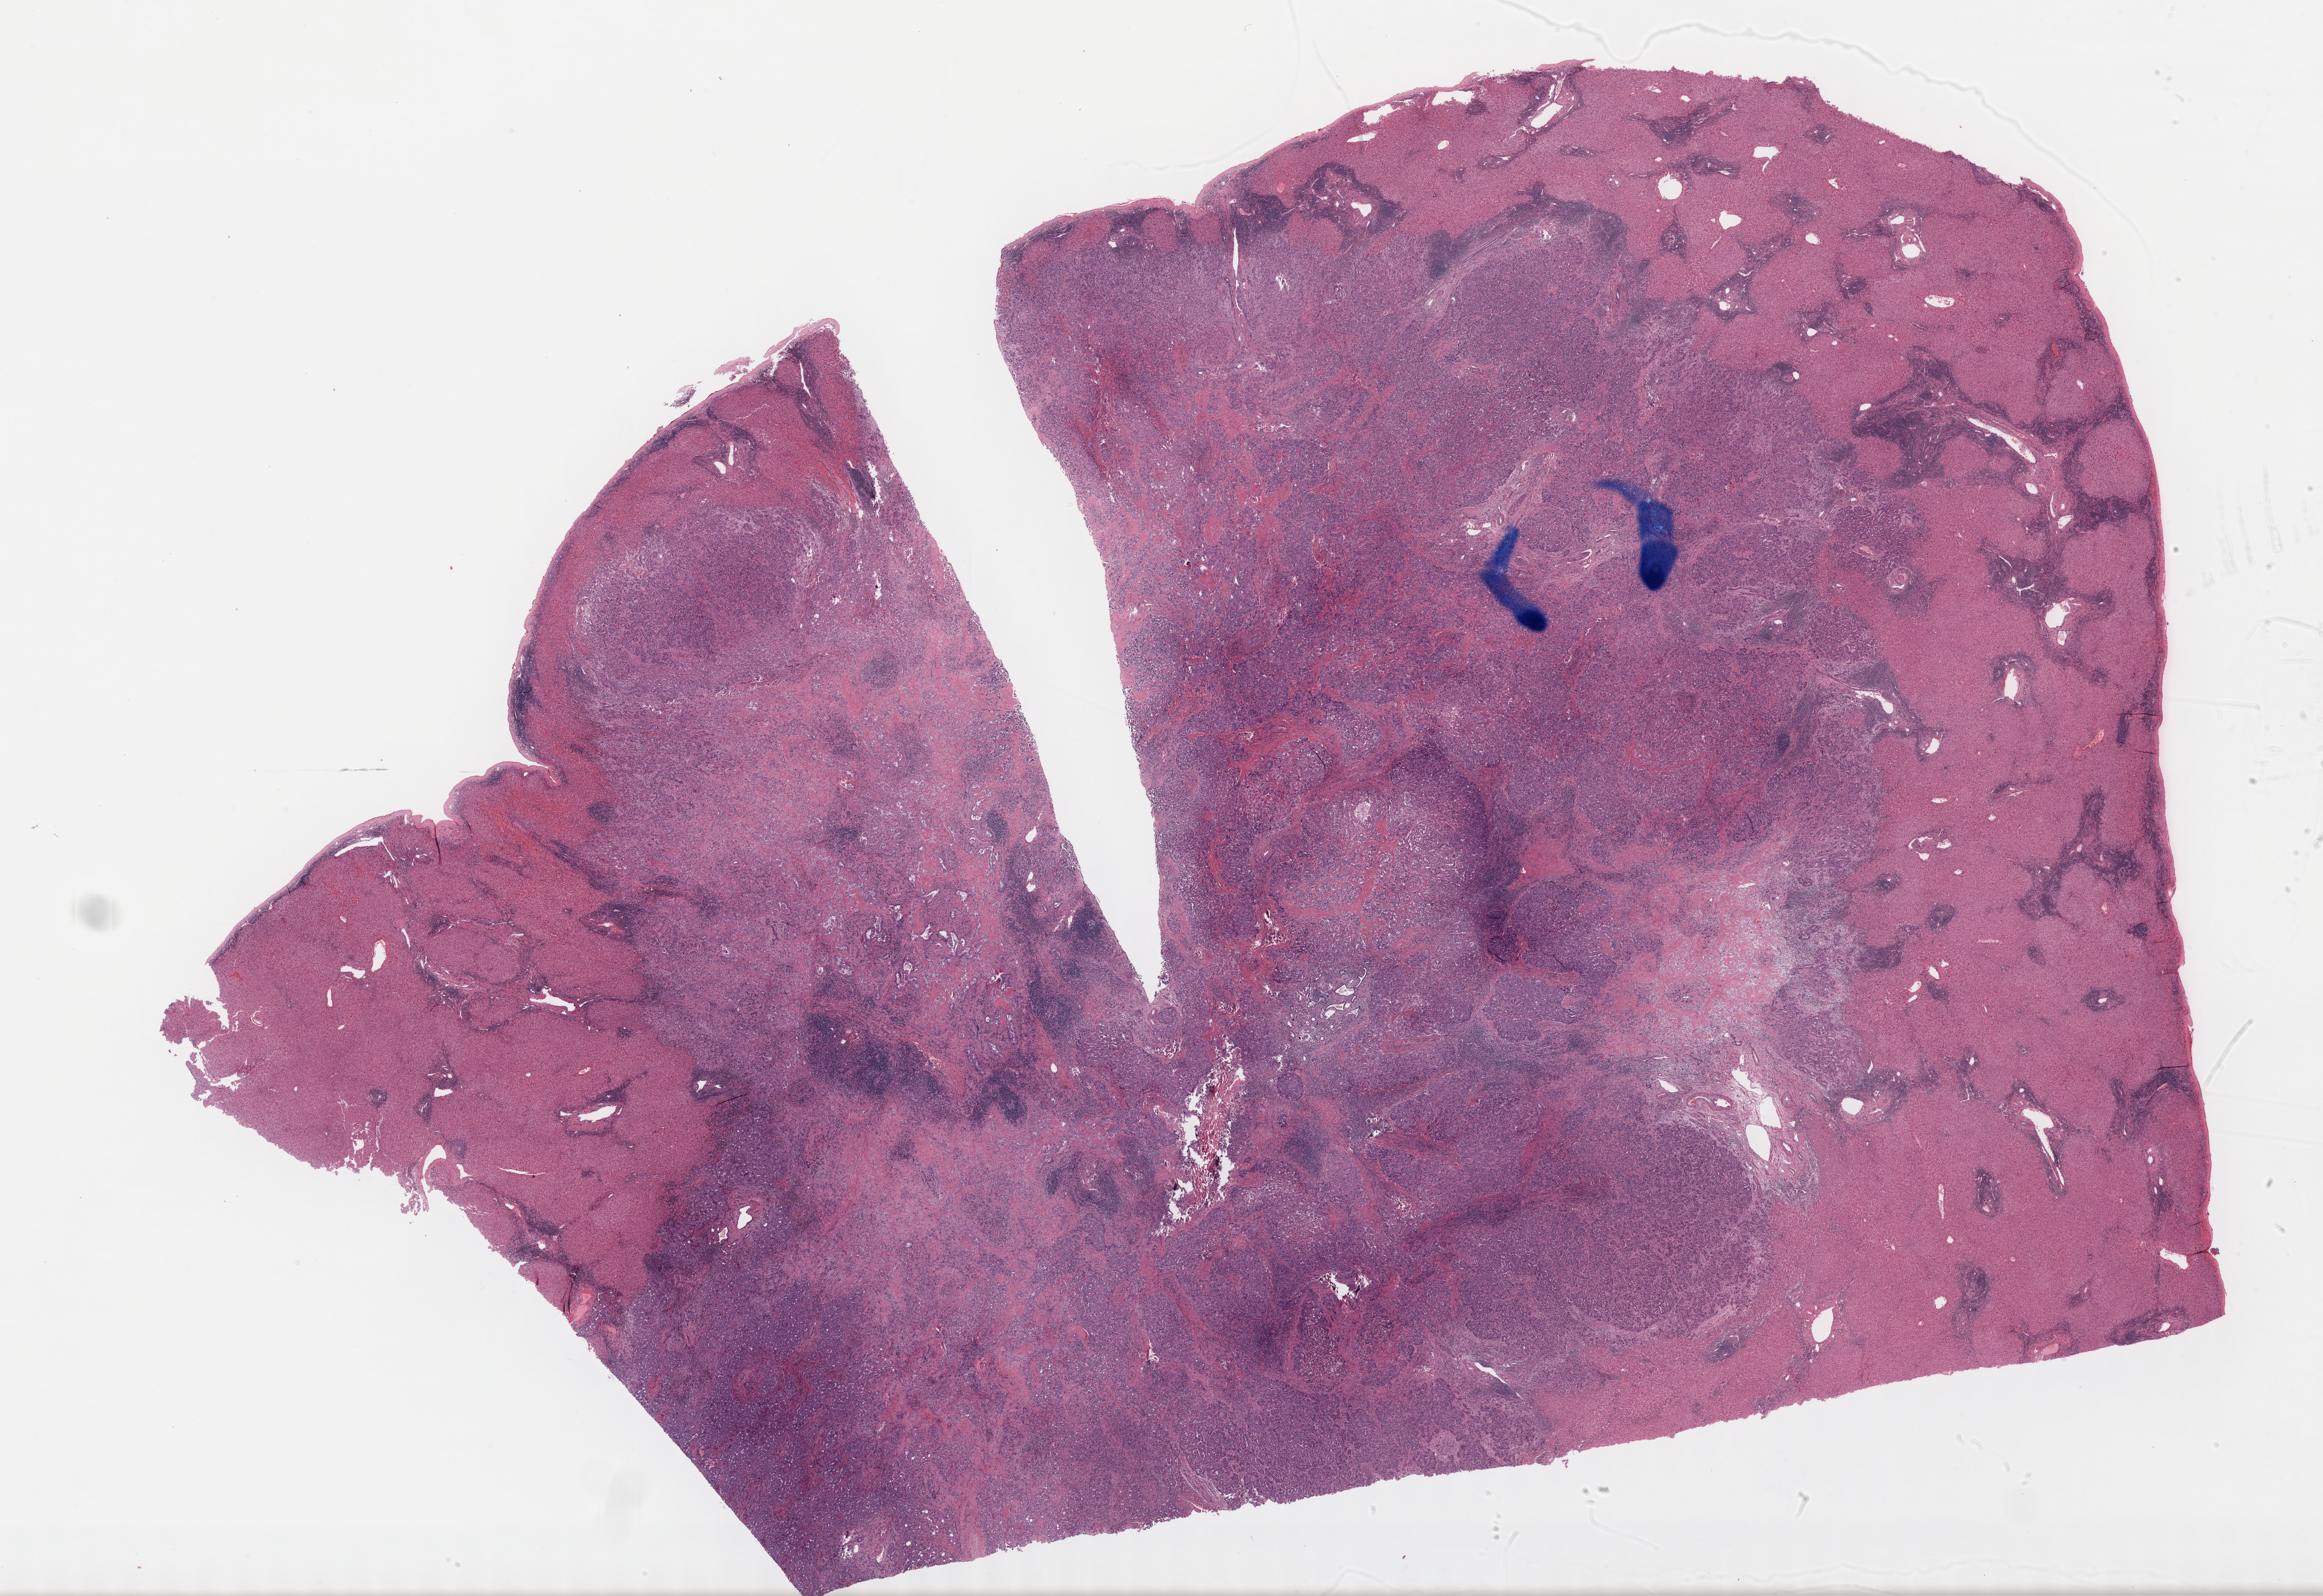
H&E-stained whole-slide image, a low-resolution overview of the entire scanned area, about 31.2 x 21.4 mm, formalin-fixed paraffin-embedded (FFPE) diagnostic section, sample: primary tumour, bile duct. Patient: male, age at initial diagnosis 60 years. Histologic grade: G2 (moderately differentiated).
AJCC pathologic stage: II (7th edition). Diagnosis: Cholangiocarcinoma (intrahepatic bile duct).